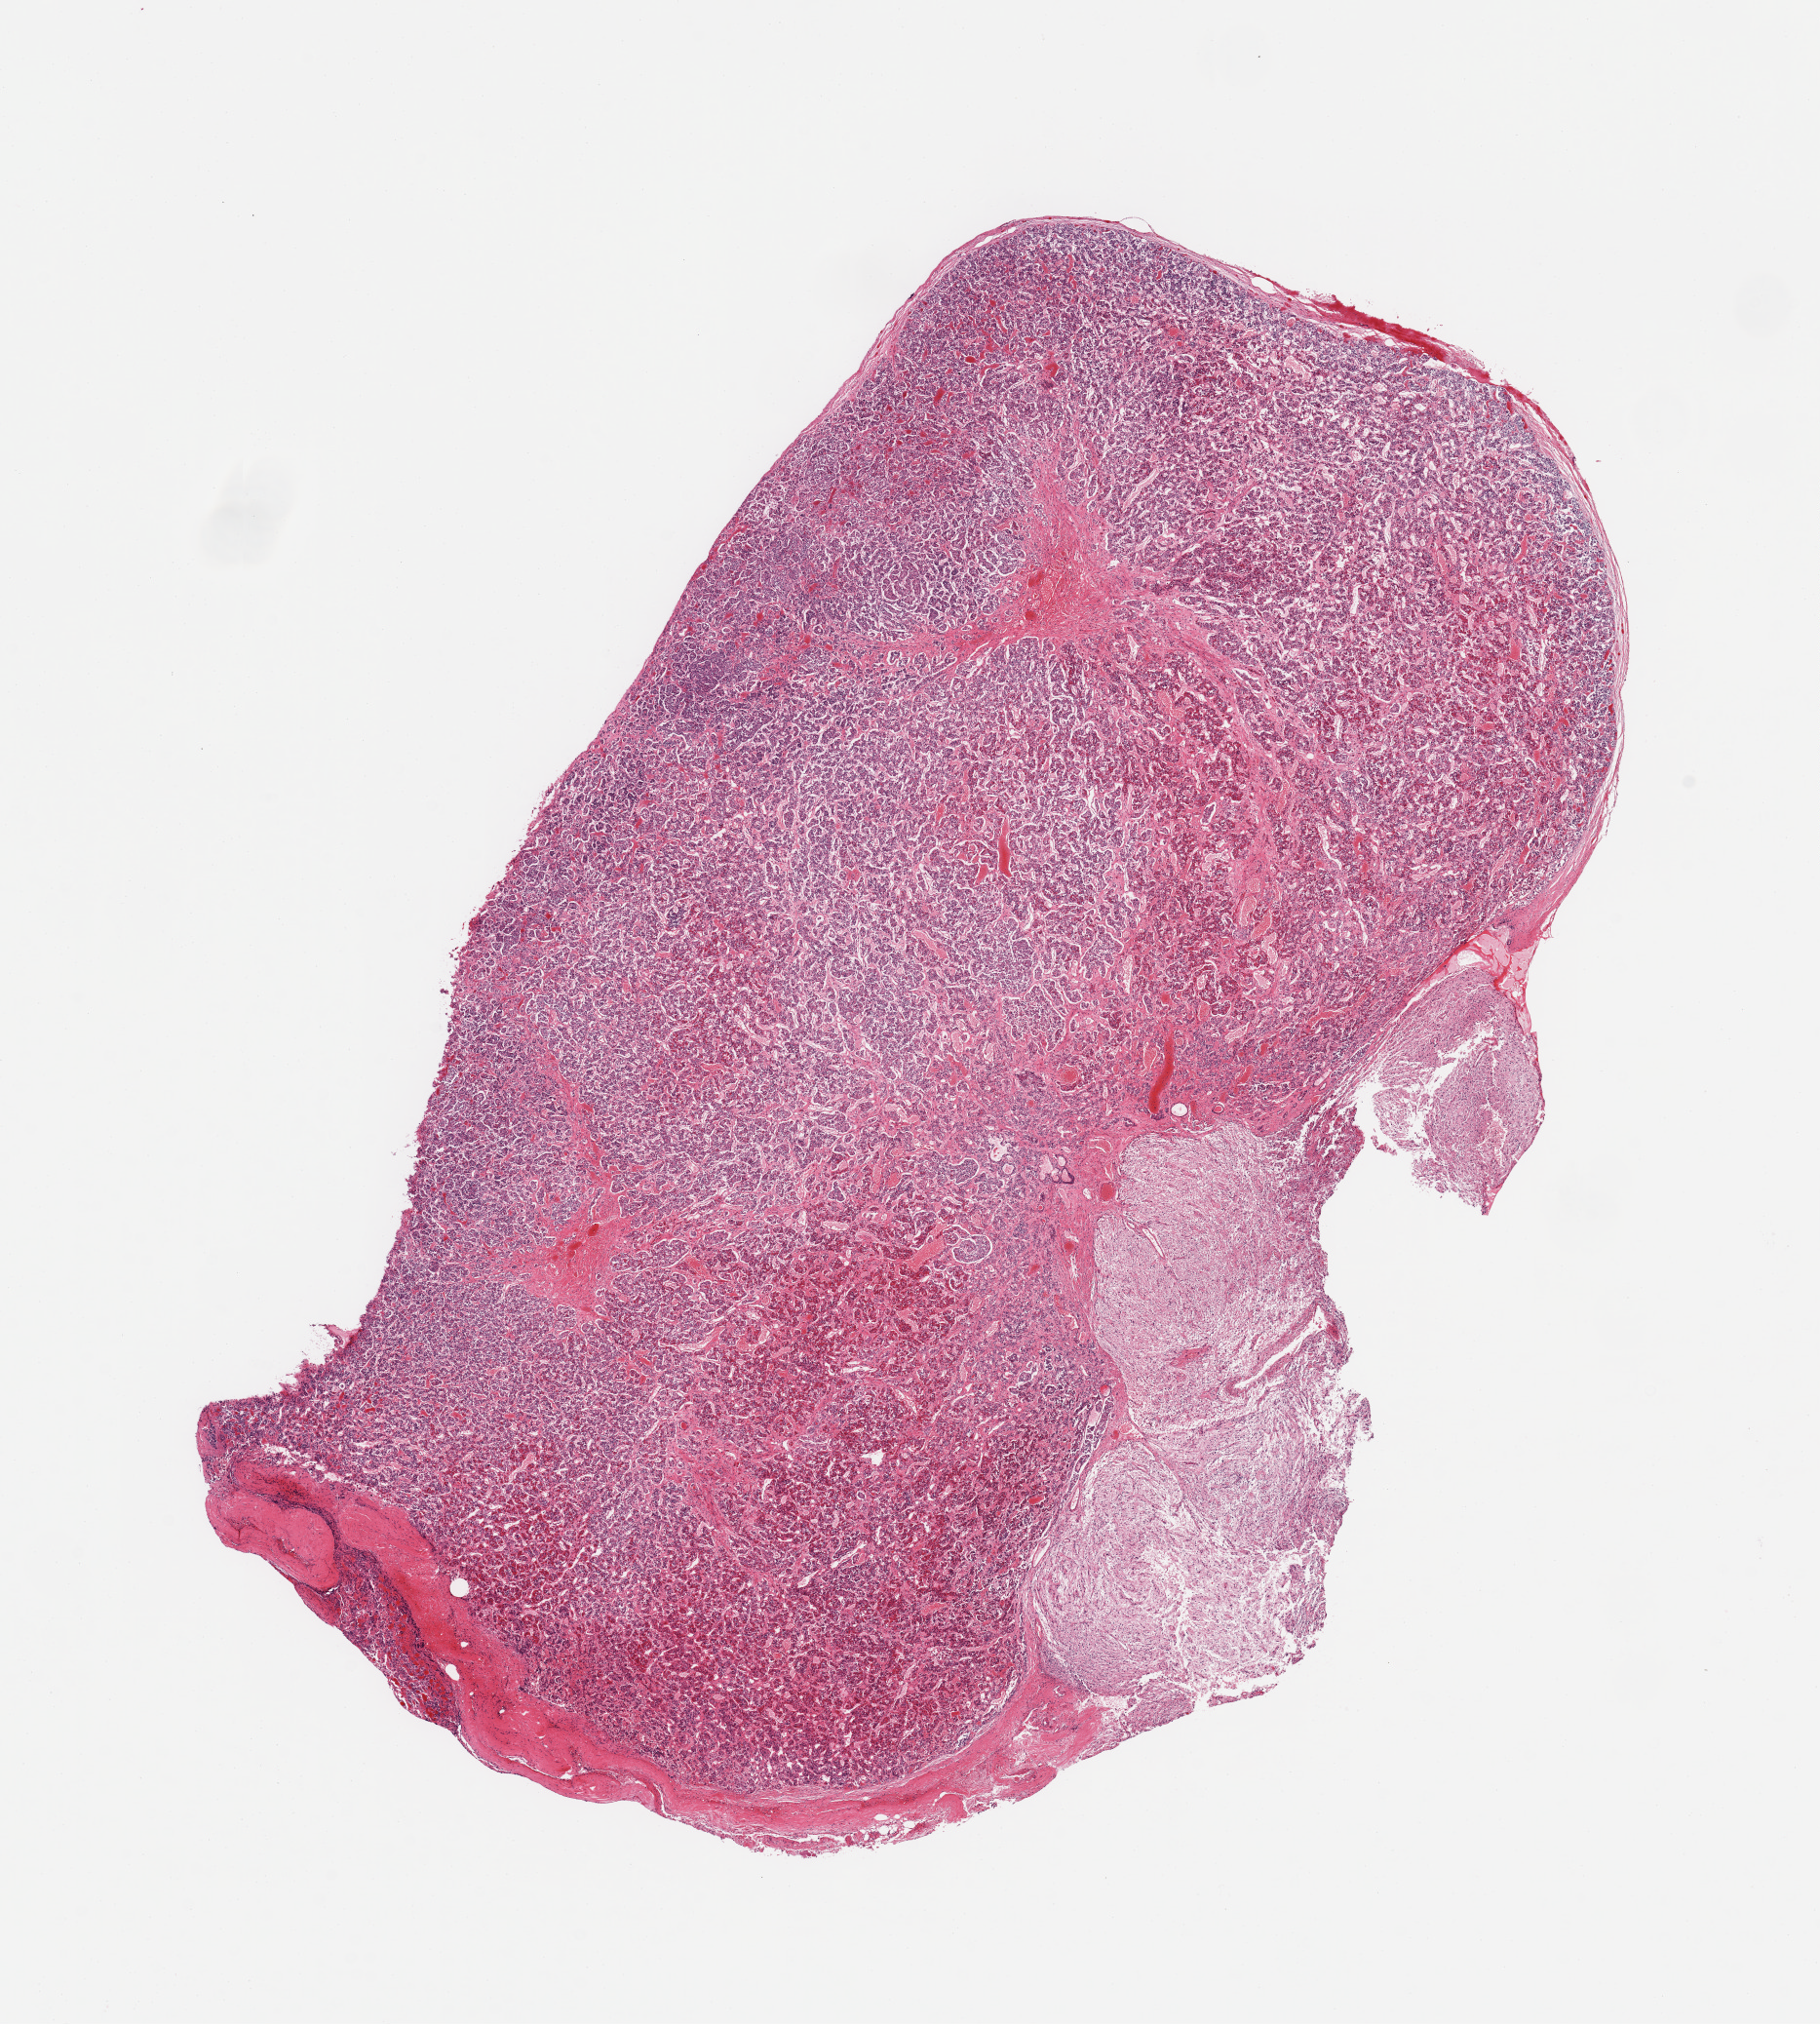
Digitized H&E-stained section — shown as a low-resolution overview of the whole scanned area (about 14.8 x 16.4 mm), PAXgene-fixed, paraffin-embedded tissue, sampled site (target tissue): pituitary, tissue donor sample. Donor: male.
- reviewer comment on this tissue sample: 1 piece; anterior lobe is 85%, posterior is 15%